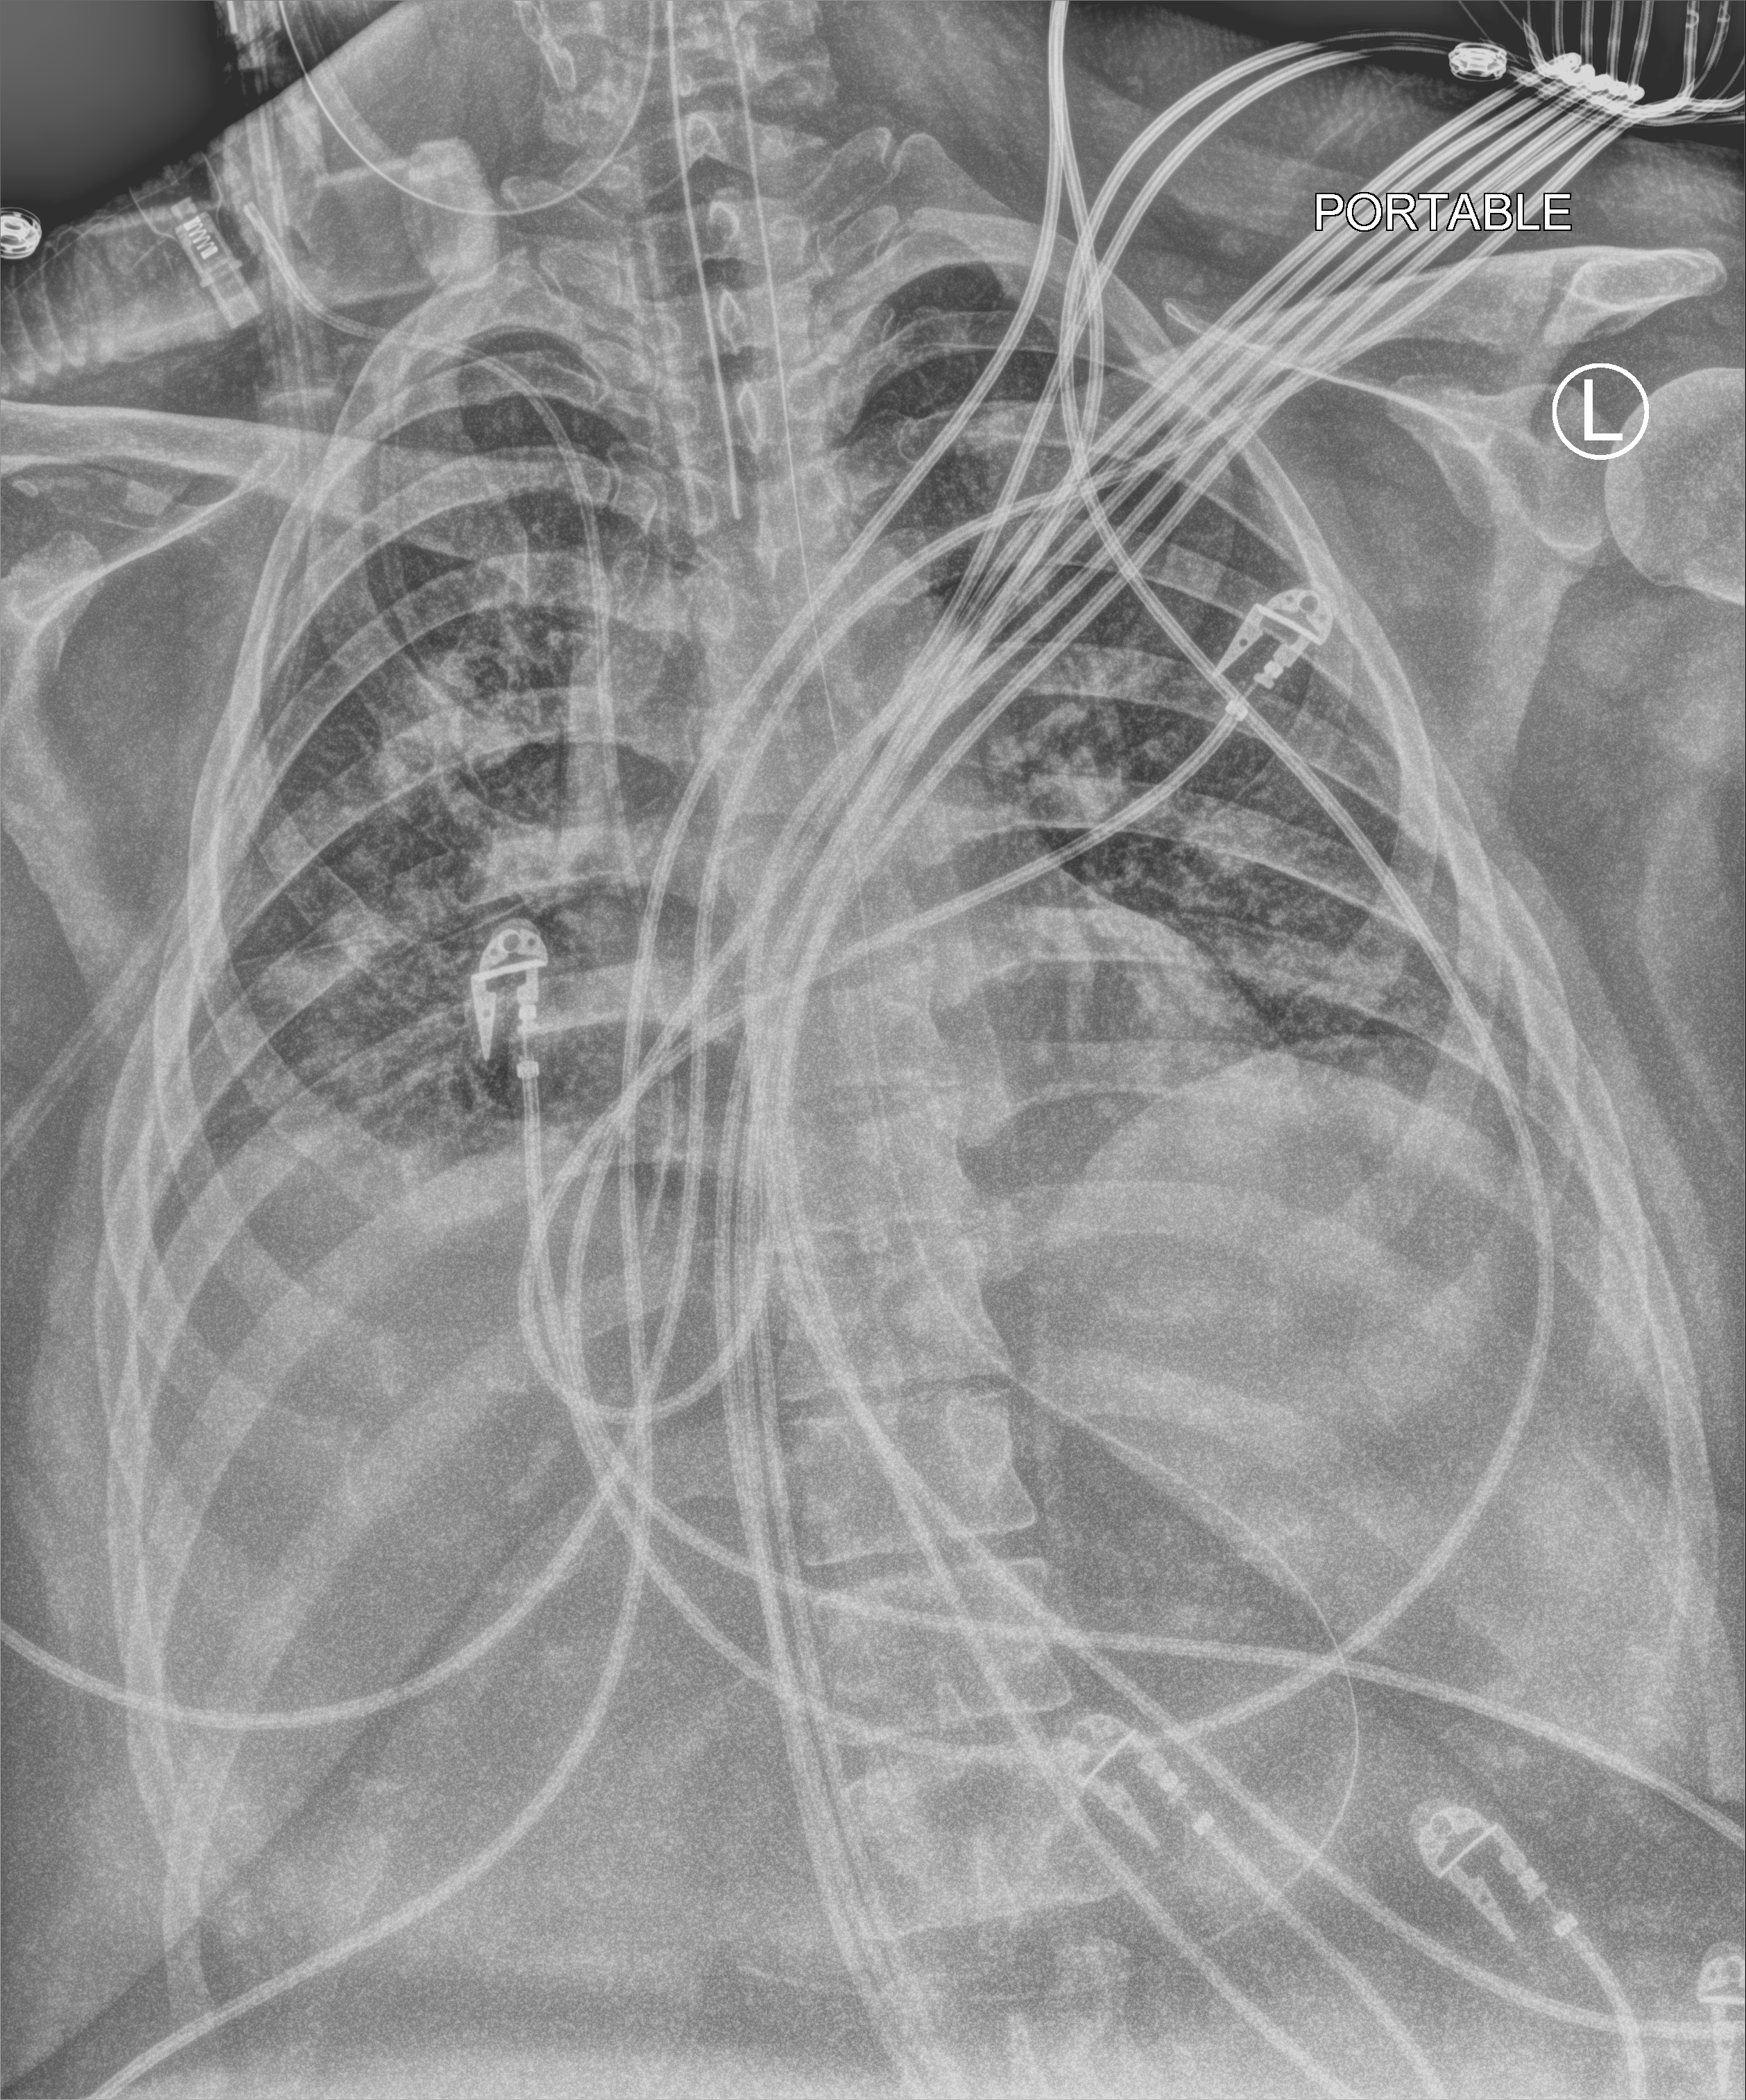
Portable chest radiograph, anteroposterior (AP) projection. Patient hospitalised with COVID-19; female, aged 18–59 years.
Hospital-stay facts (about this admission, not read from this image; timing relative to this image not recorded):
- length of hospital stay: 25 days